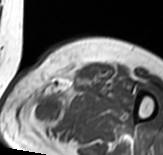
MRI of an extremity soft-tissue mass, one axial slice; position 48 of 65 along the scan axis; MR volume resampled by the dataset authors to the PET/CT grid (not the native acquisition matrix); 163 × 155 image matrix, field of view 159 × 151 mm. Female patient. Case-level facts recorded for this patient, not image findings: histological type: pleomorphic leiomyosarcoma; grade: high; site of the primary tumour: left thigh.
Outlined on this slice (expert contour drawn on MRI and transferred to this co-registered scan by the dataset authors):
- gross tumour volume including surrounding oedema: bounding box [x1, y1, x2, y2] px = [26, 67, 90, 134]